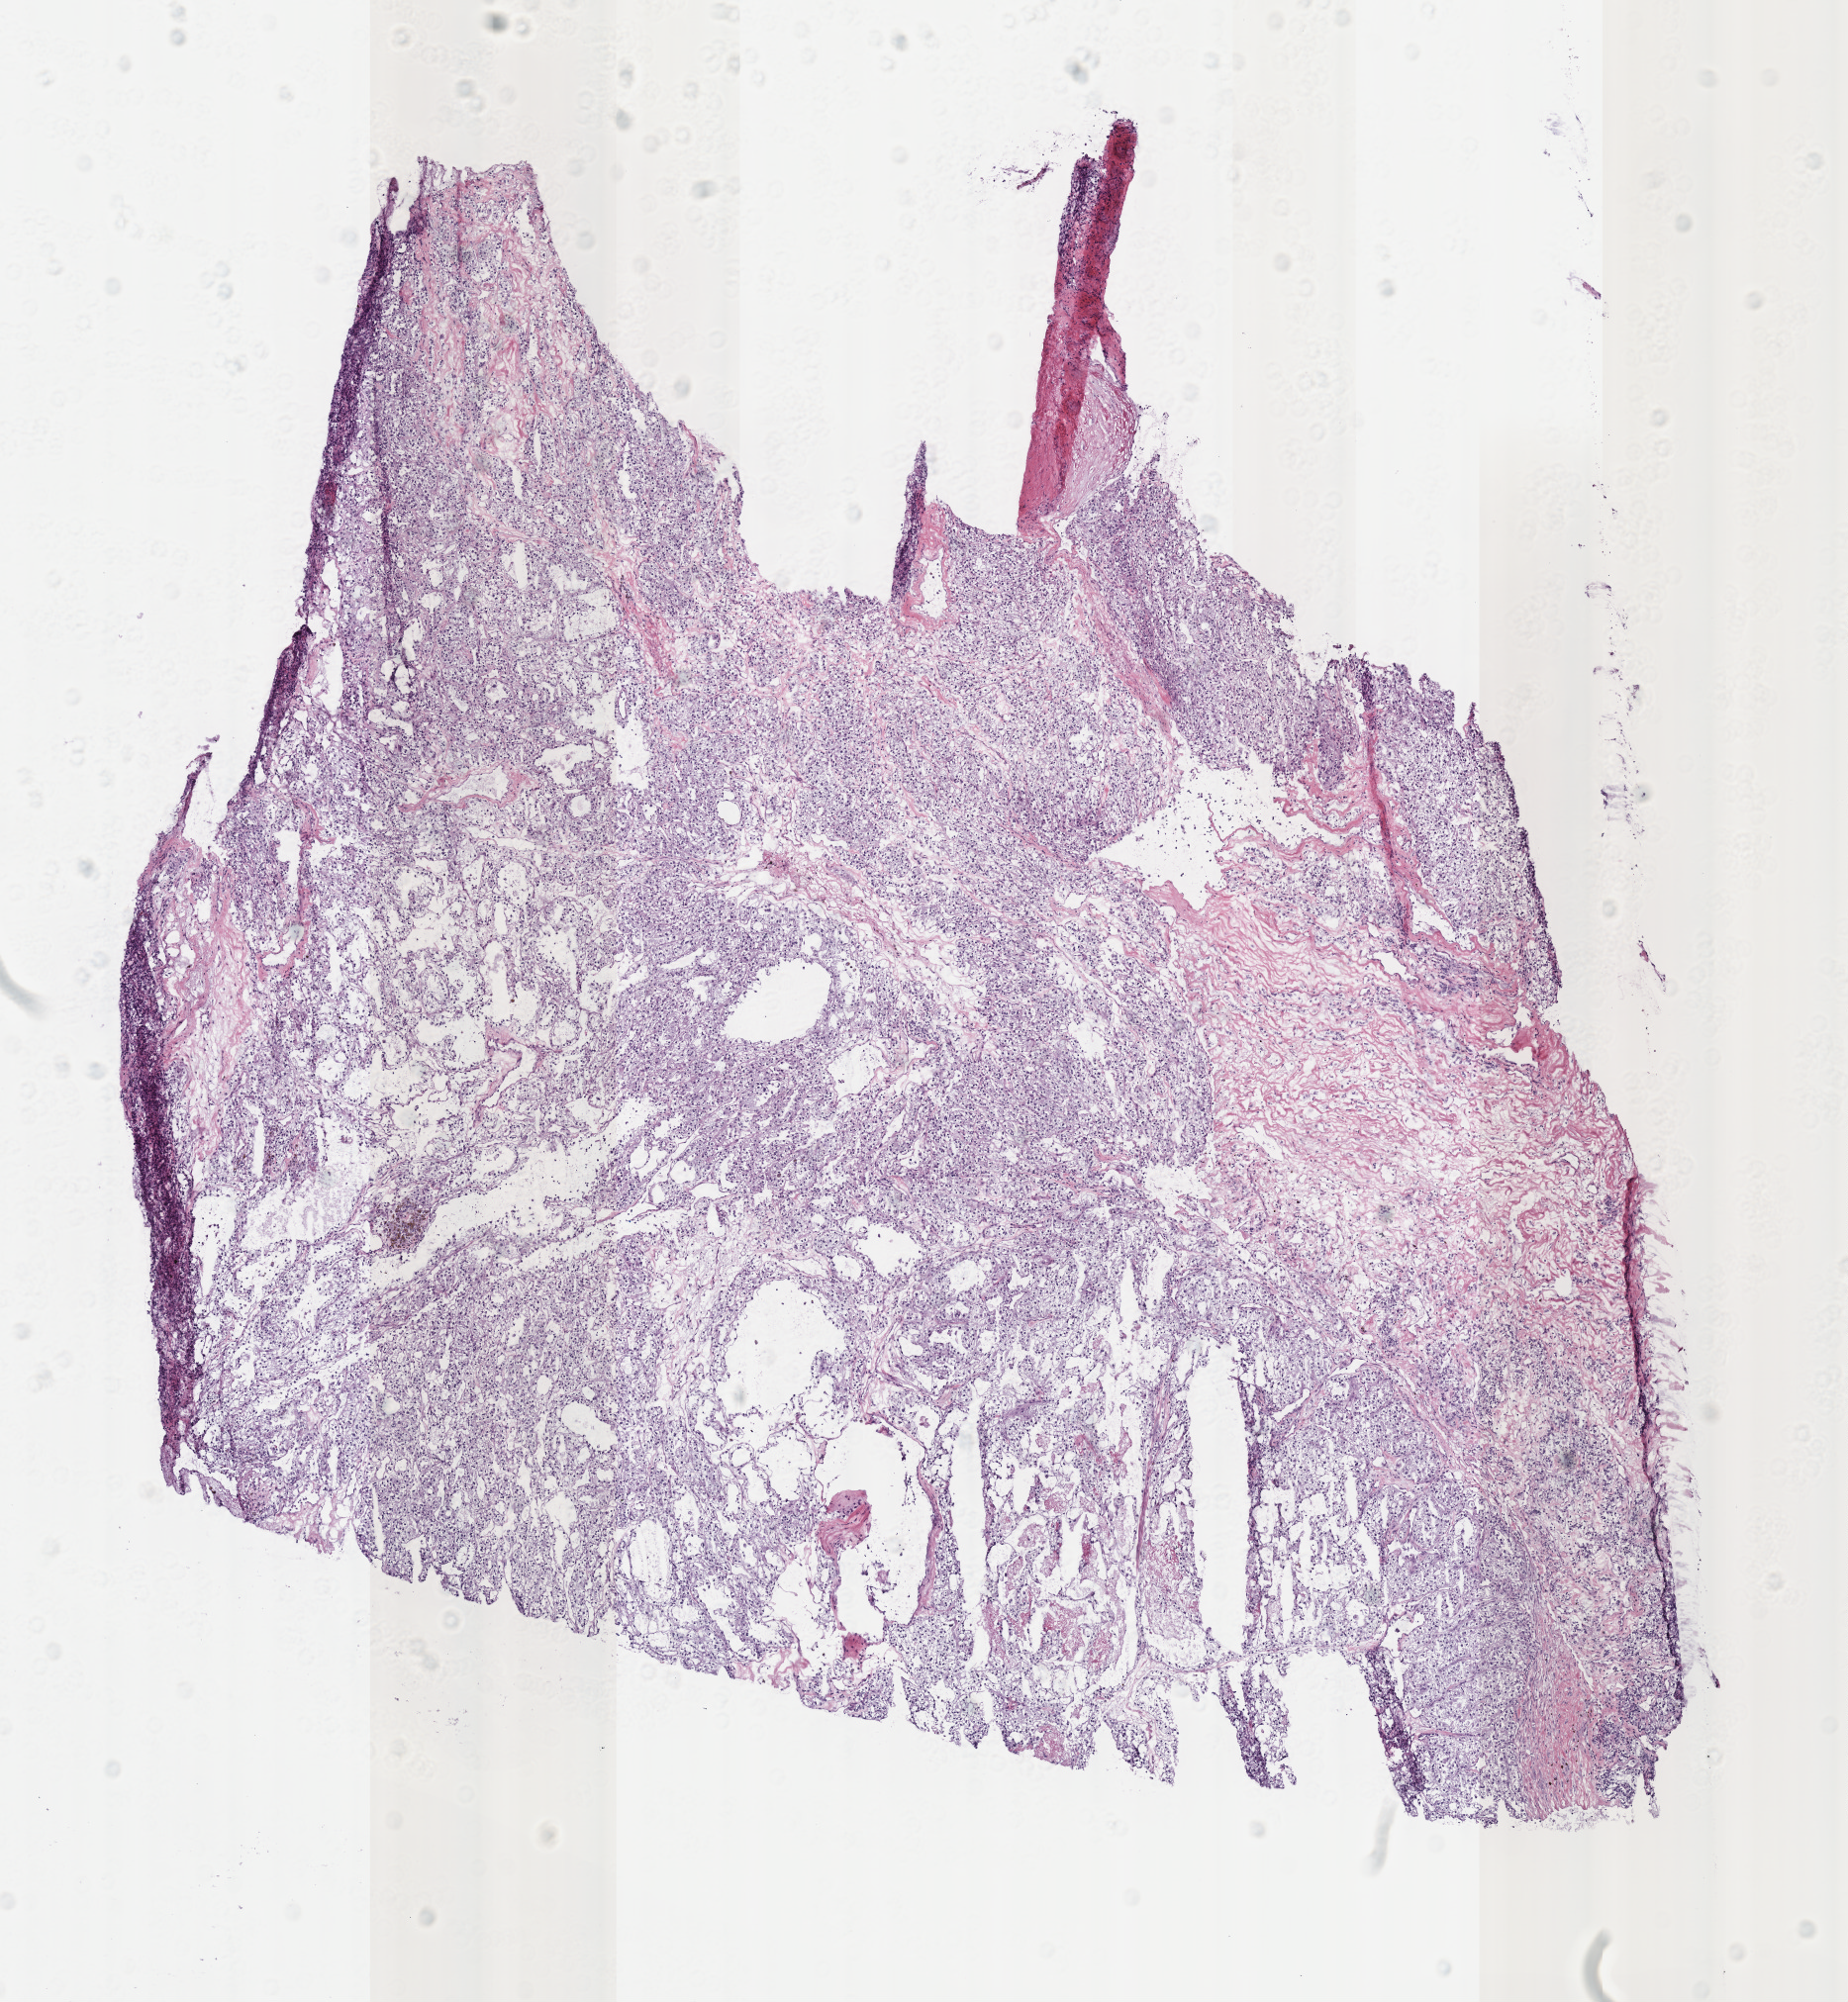
Digitized Hematoxylin and eosin (H&E) stained tissue section (whole slide) — whole scanned area (about 7.3 x 8.0 mm, acquisition: 40x scan) shown as a low-resolution overview, frozen section from the bottom of the tissue portion, sample: primary tumour, kidney. Male patient; age at initial diagnosis 53 years. Slide review estimates, as recorded: tumour cells 85%, tumour nuclei 85%.
Diagnosis: Clear cell adenocarcinoma, NOS.